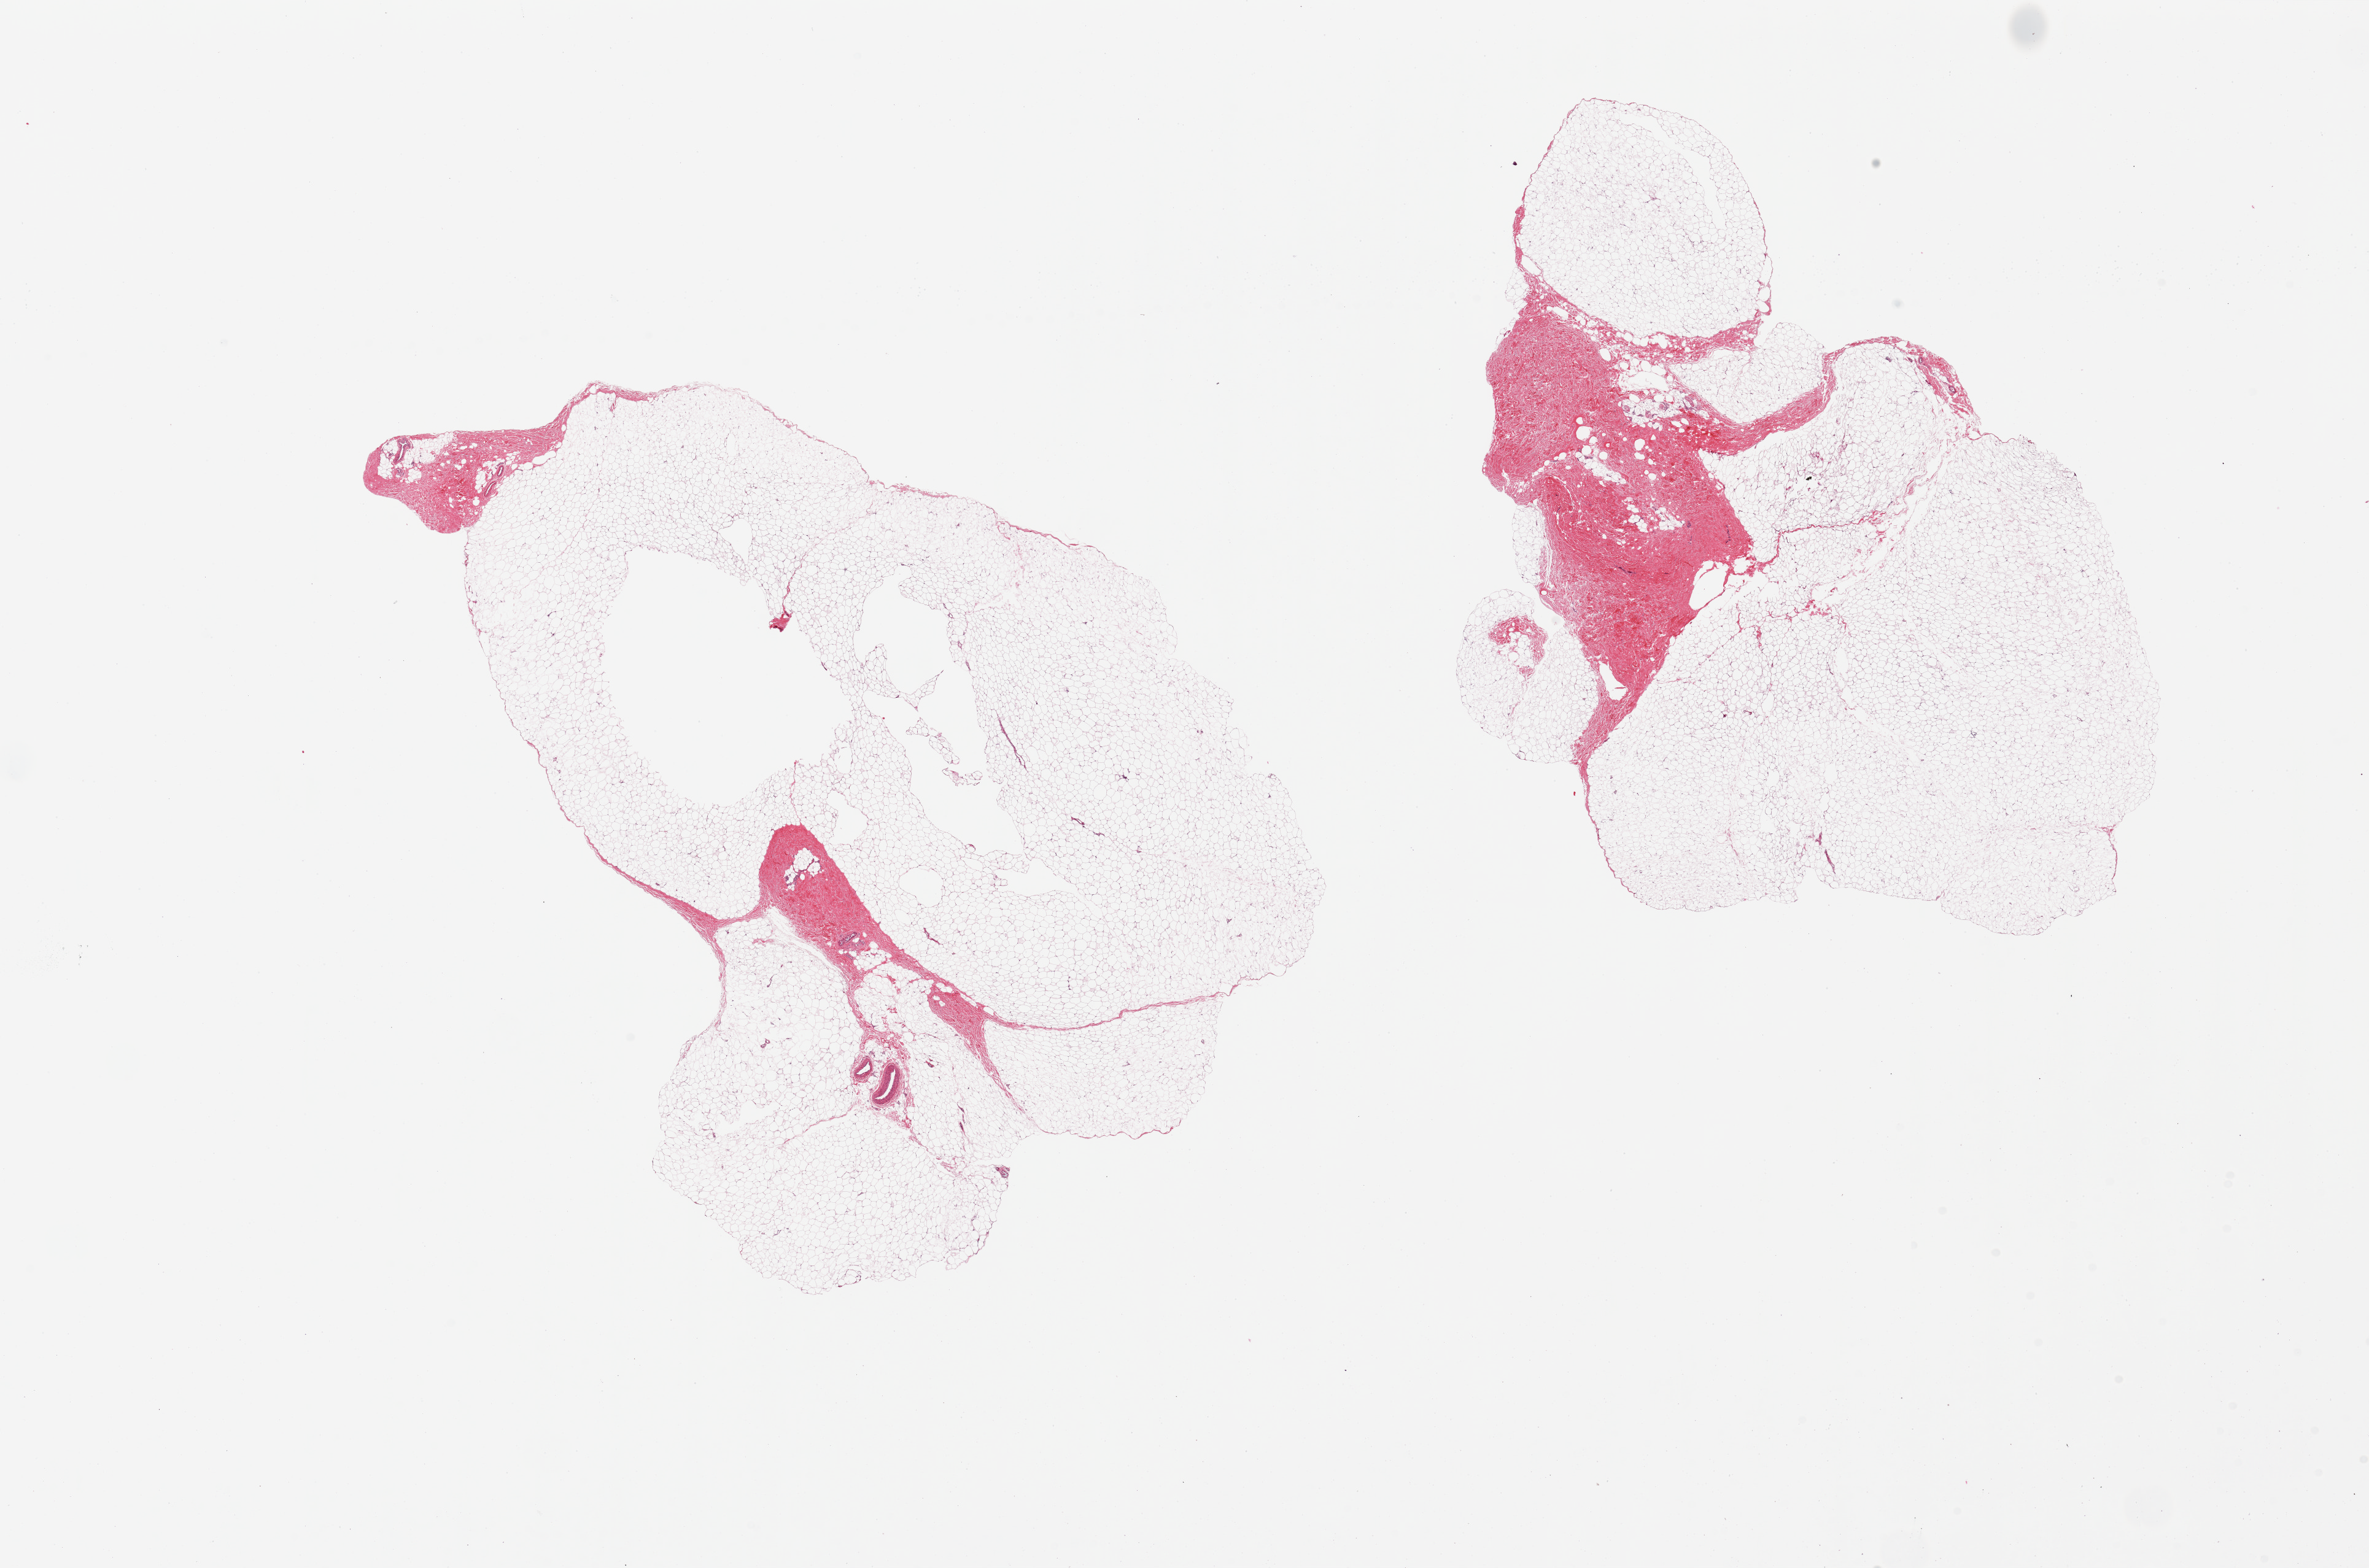
H&E whole-slide image, brightfield, whole scanned area (about 30.5 x 20.2 mm) shown as a low-resolution overview; PAXgene-fixed, paraffin-embedded tissue; sampled site (target tissue): breast; donor tissue sample. Donor: male.
Reviewer comment on this tissue sample: 2 pieces, adipose and fibrous tissue, no ductal elements present.